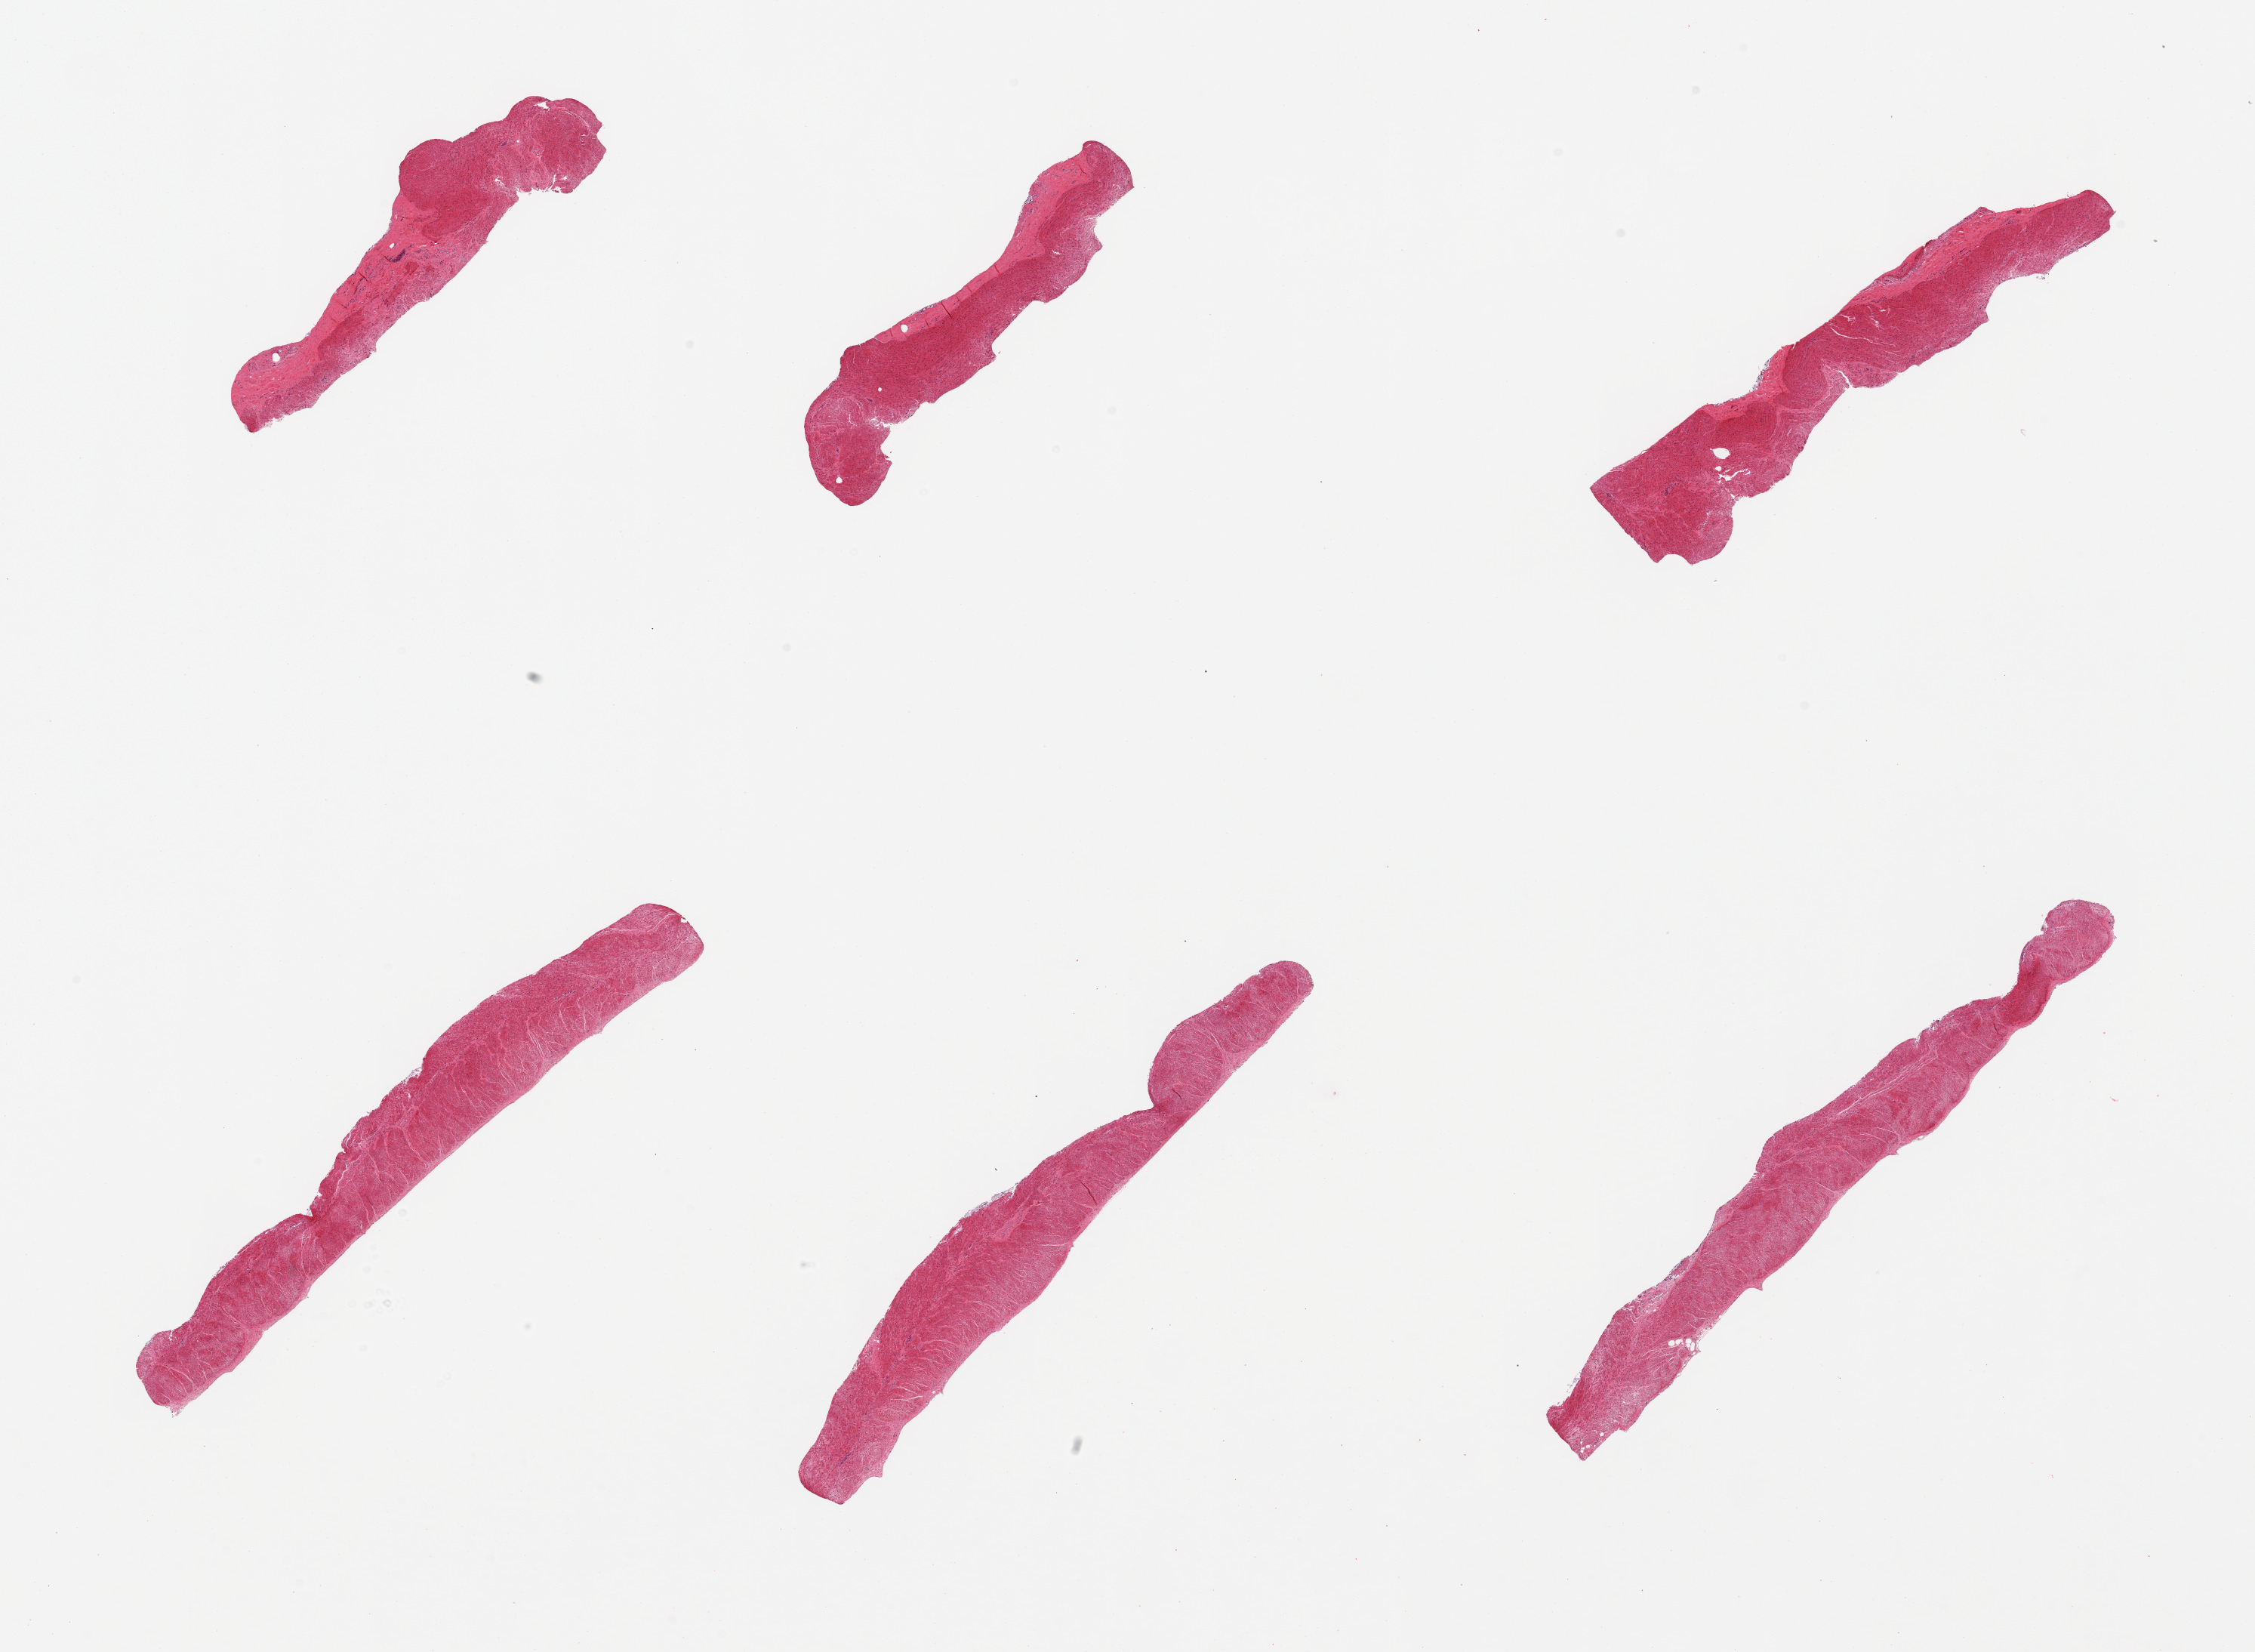
Haematoxylin and eosin whole-slide image — shown as a low-resolution overview of the whole scanned area (about 23.6 x 17.3 mm), PAXgene-fixed paraffin-embedded (PFPE) section, target tissue: sigmoid colon, tissue donor sample. Donor sex: male.
* pathologist's review note for this sample: 6 pieces, unusually advanced autolysis